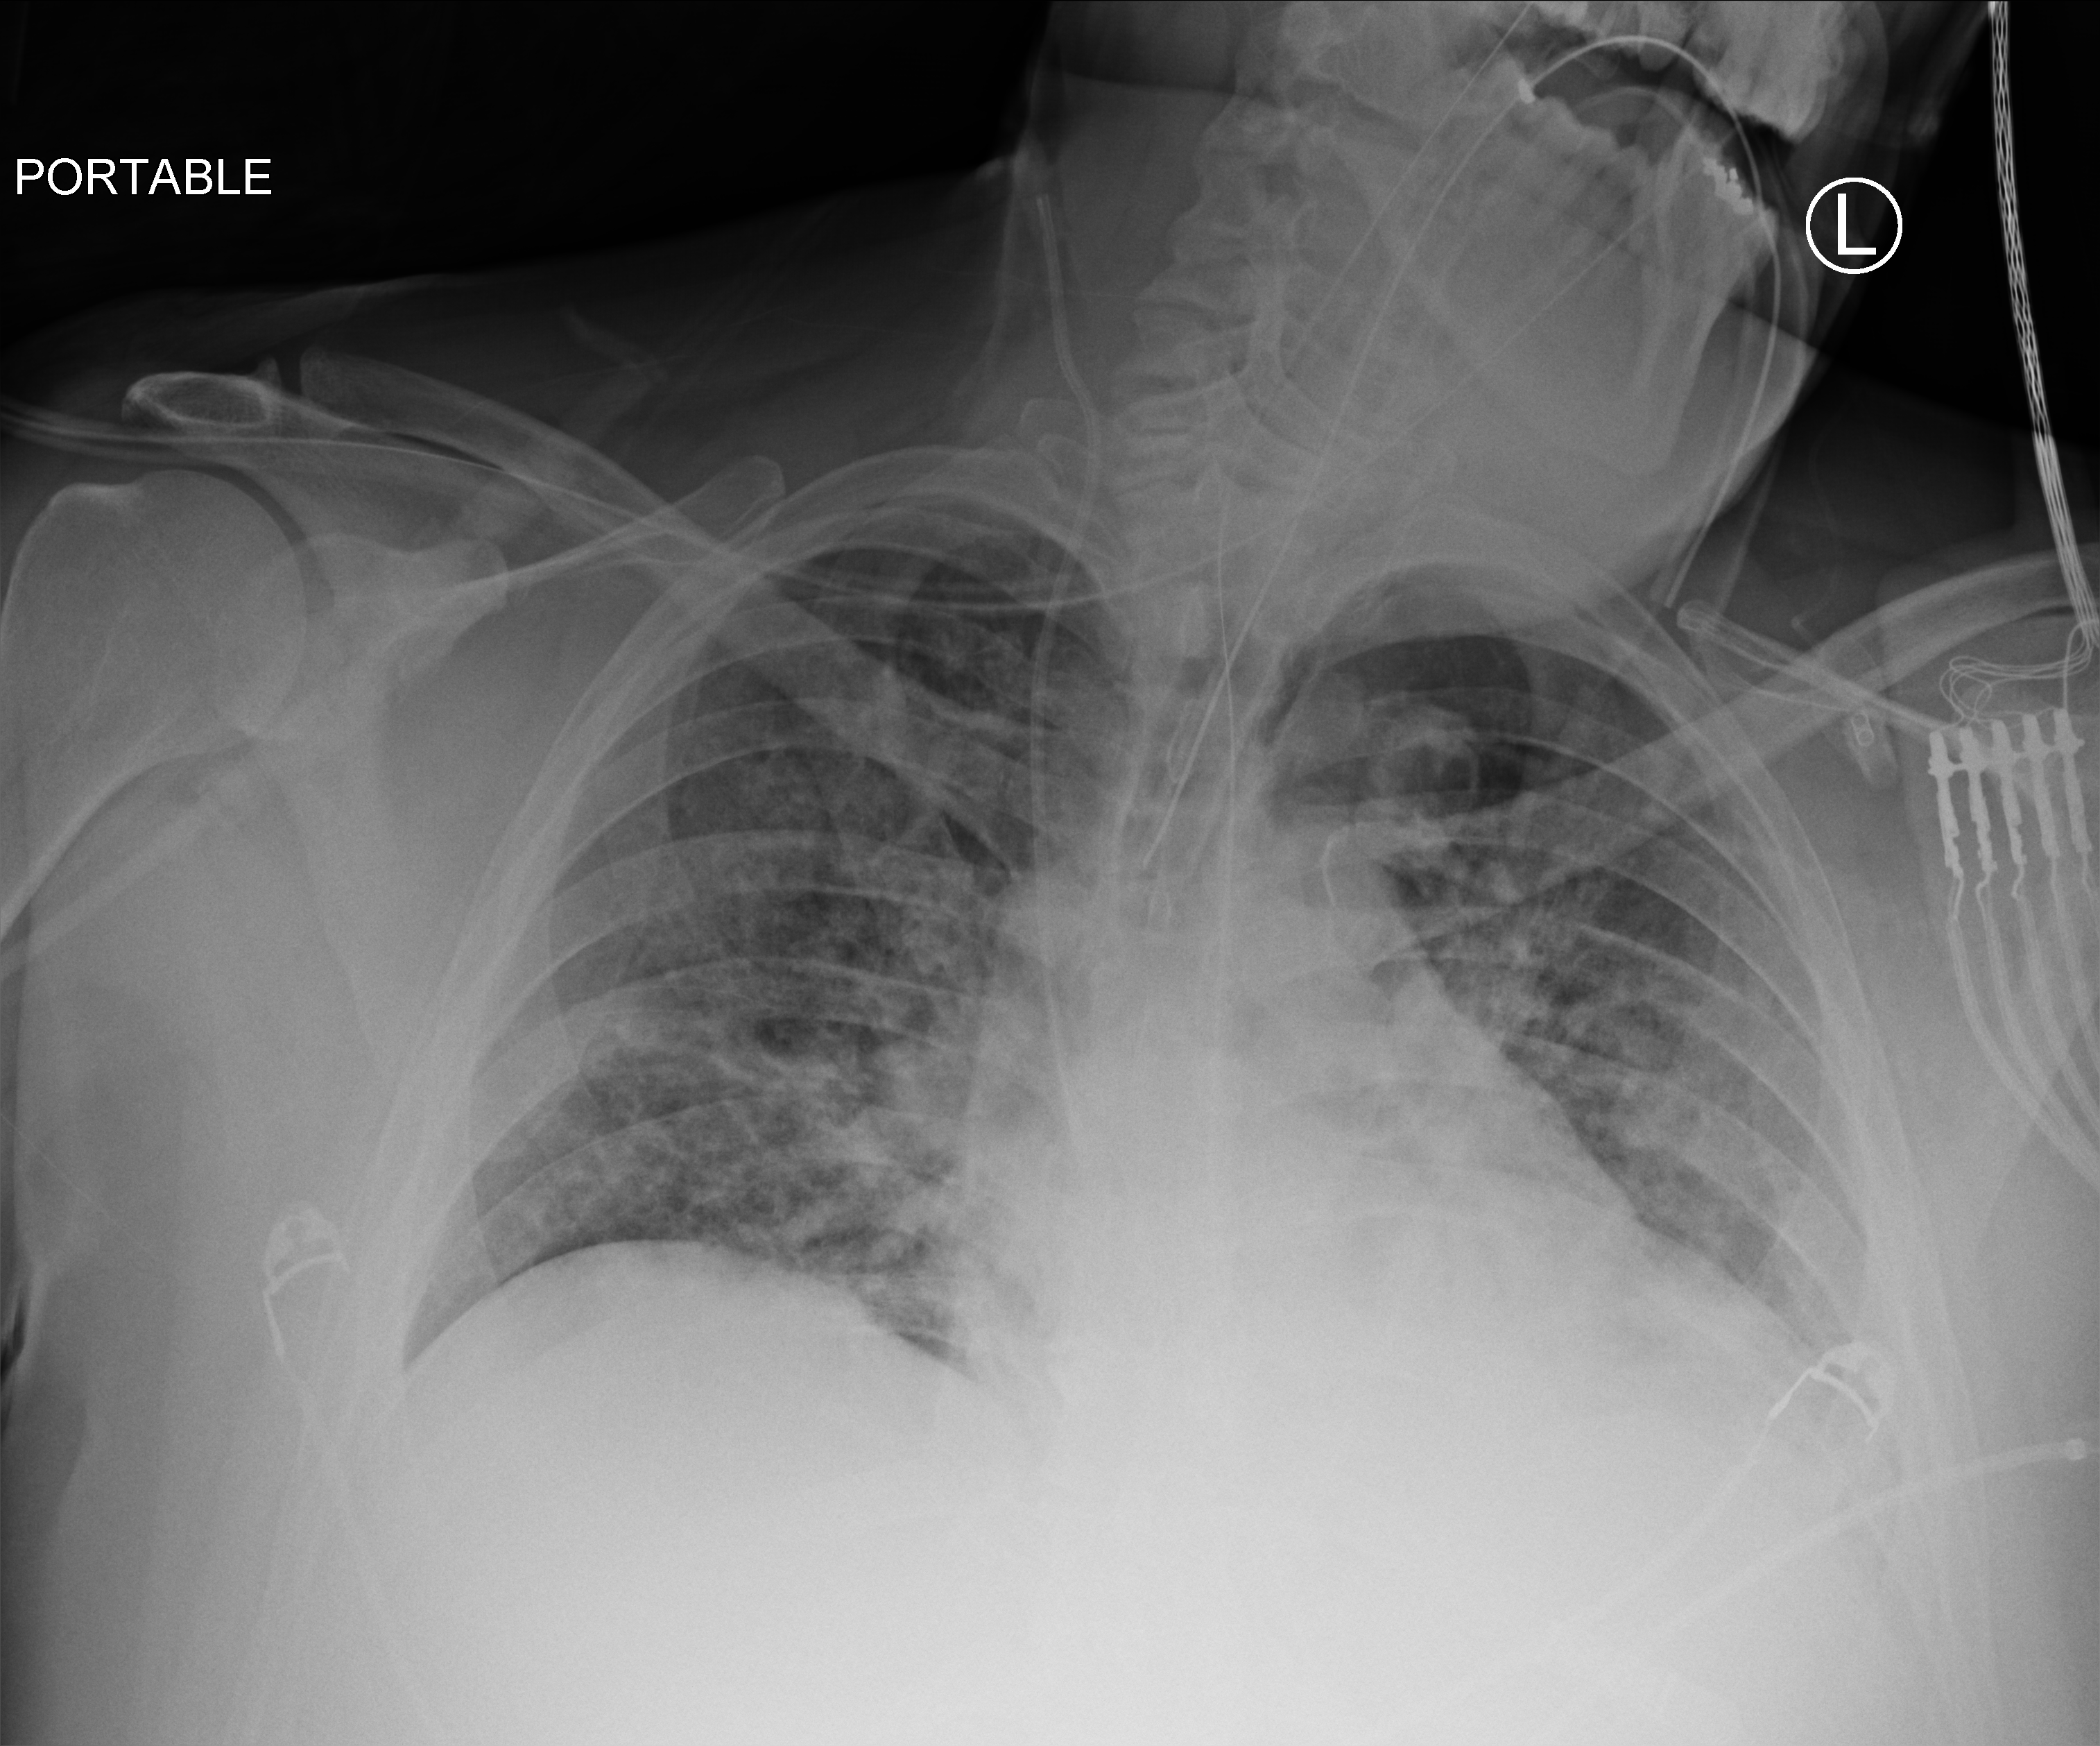
Portable chest radiograph, anteroposterior (AP) projection. Male patient hospitalised with COVID-19, age 18–59 years.
Hospital-stay facts (about this admission, not read from this image; timing relative to this image not recorded): diabetes (admission record): no; mechanically ventilated during this hospital stay: yes; admitted to intensive care during this hospital stay: yes.